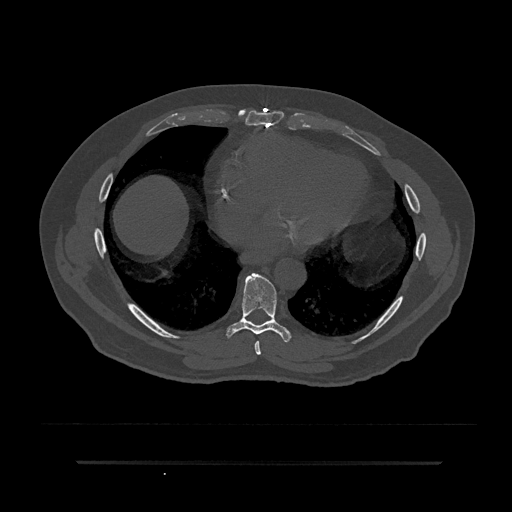
CT including the spine, one axial slice. Slice 431 of 797 in the series (ordered by position). Reconstruction kernel Br40s/3. 120 kVp. Bone window (W 1800 / L 400 HU). 0.5 mm slice thickness. 512 × 512 image matrix, field of view 464 × 464 mm. Patient: male, 59 years. Case-level facts recorded for this patient, not image findings: primary cancer: bile ducts.
Outlined on this slice (semi-automatic segmentation, software-assisted and operator-edited):
- T7 vertebra: bounding box (x1, y1, x2, y2) in pixels: (254, 341, 261, 355)
- T8 vertebra: (226, 273, 291, 343)